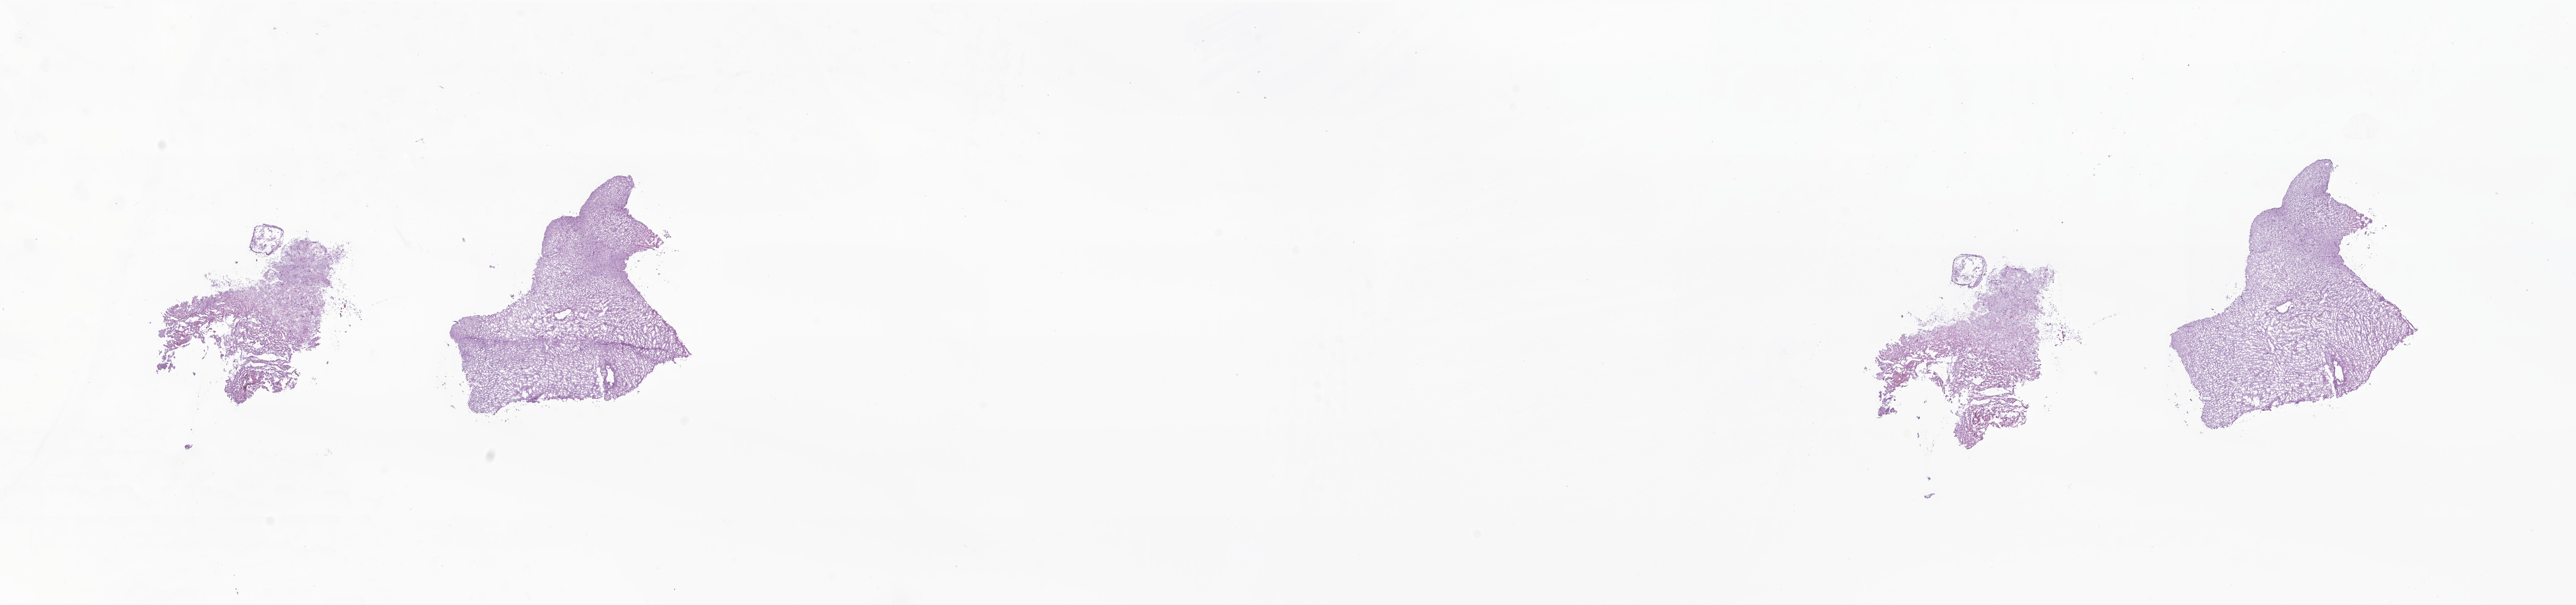
H&E whole-slide image of tumor tissue from the brain, low-resolution overview of the scanned area, about 30.3 x 7.1 mm. Frozen section. Patient: male, age 139 months (11 years 7 months).
• recorded diagnosis: Pilocytic astrocytoma